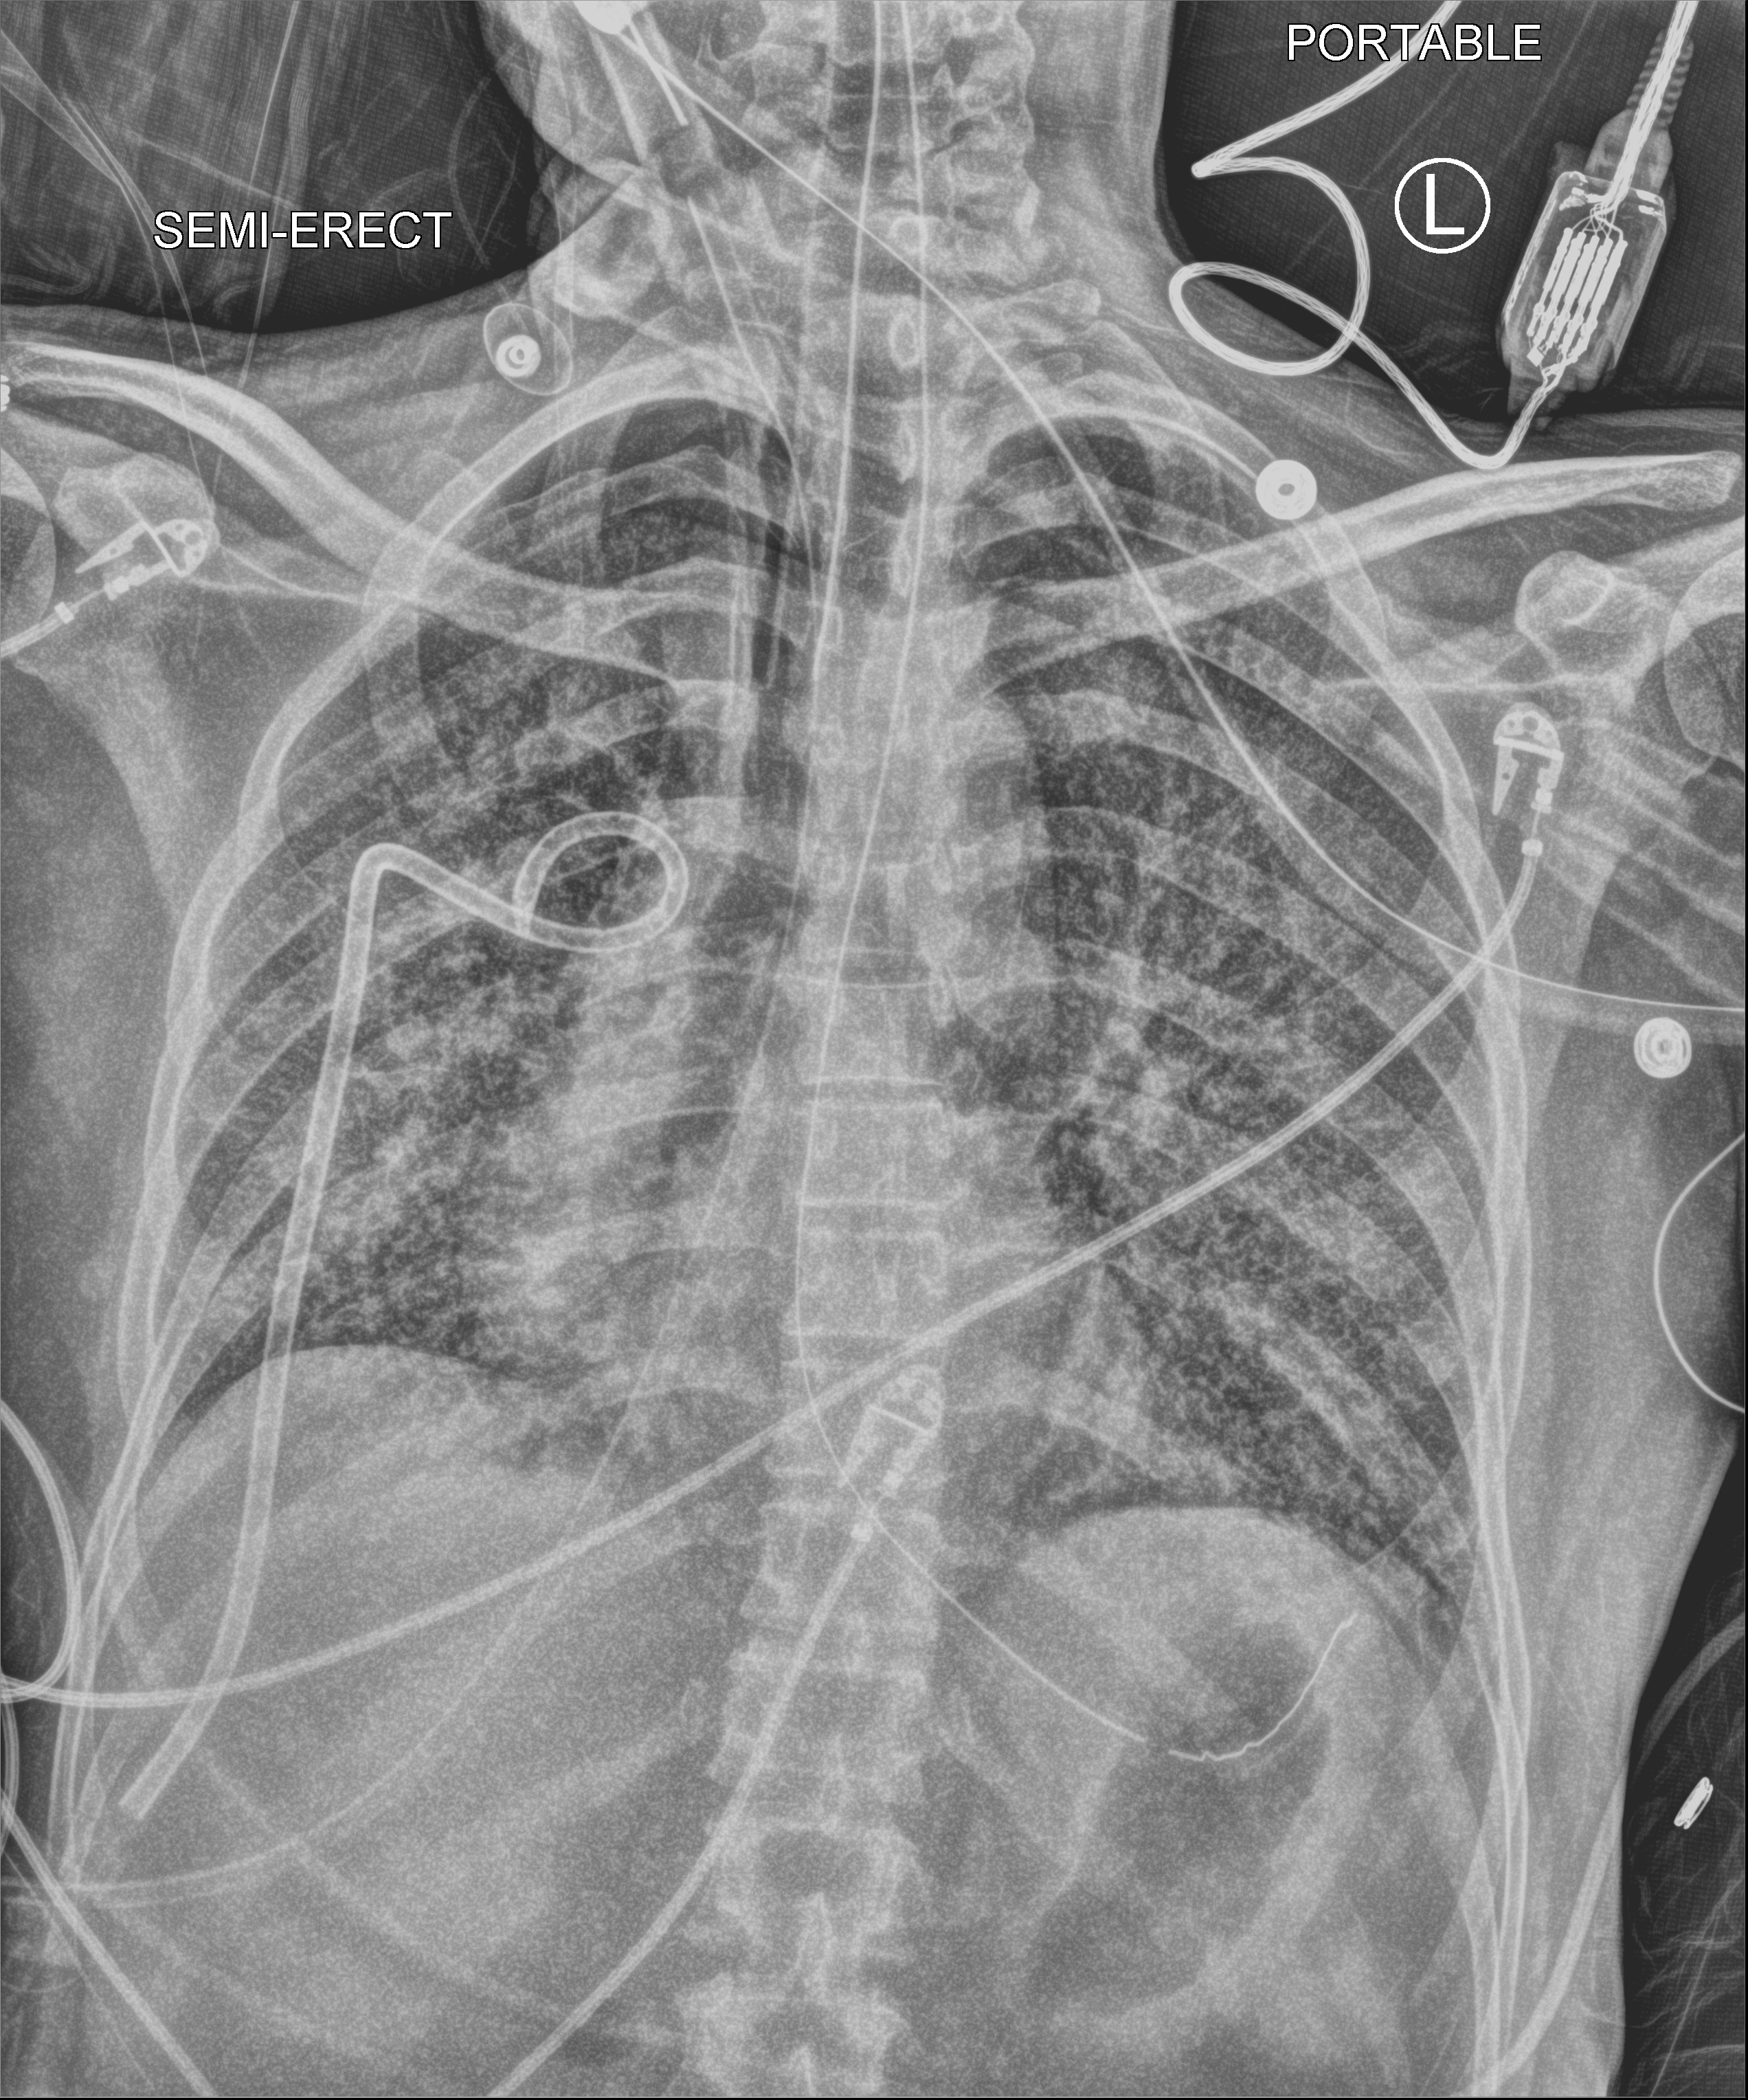
Bedside chest radiograph (computed radiography); anteroposterior (AP) projection. Adult patient hospitalised with COVID-19, age 18–59 years.
From the hospital-stay record, not from the radiograph (when in the stay this image was taken is not recorded): smoking status (admission record): never; admitted to intensive care during this hospital stay: yes.